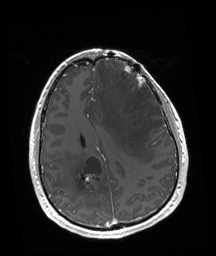
Brain MRI from a brain-tumour surgery series, one axial slice; slice 64 of 192 in the series (ordered by position); T1-weighted post-contrast; 1 mm slice thickness; 216 × 256 image matrix, field of view 219 × 260 mm. Case-level facts recorded for this patient, not image findings: tumour location: Left Frontal.
Structures marked on this image (outlined manually by an expert reader):
- tumour: bounding box <123,66,145,88> (left, top, right, bottom; pixels)